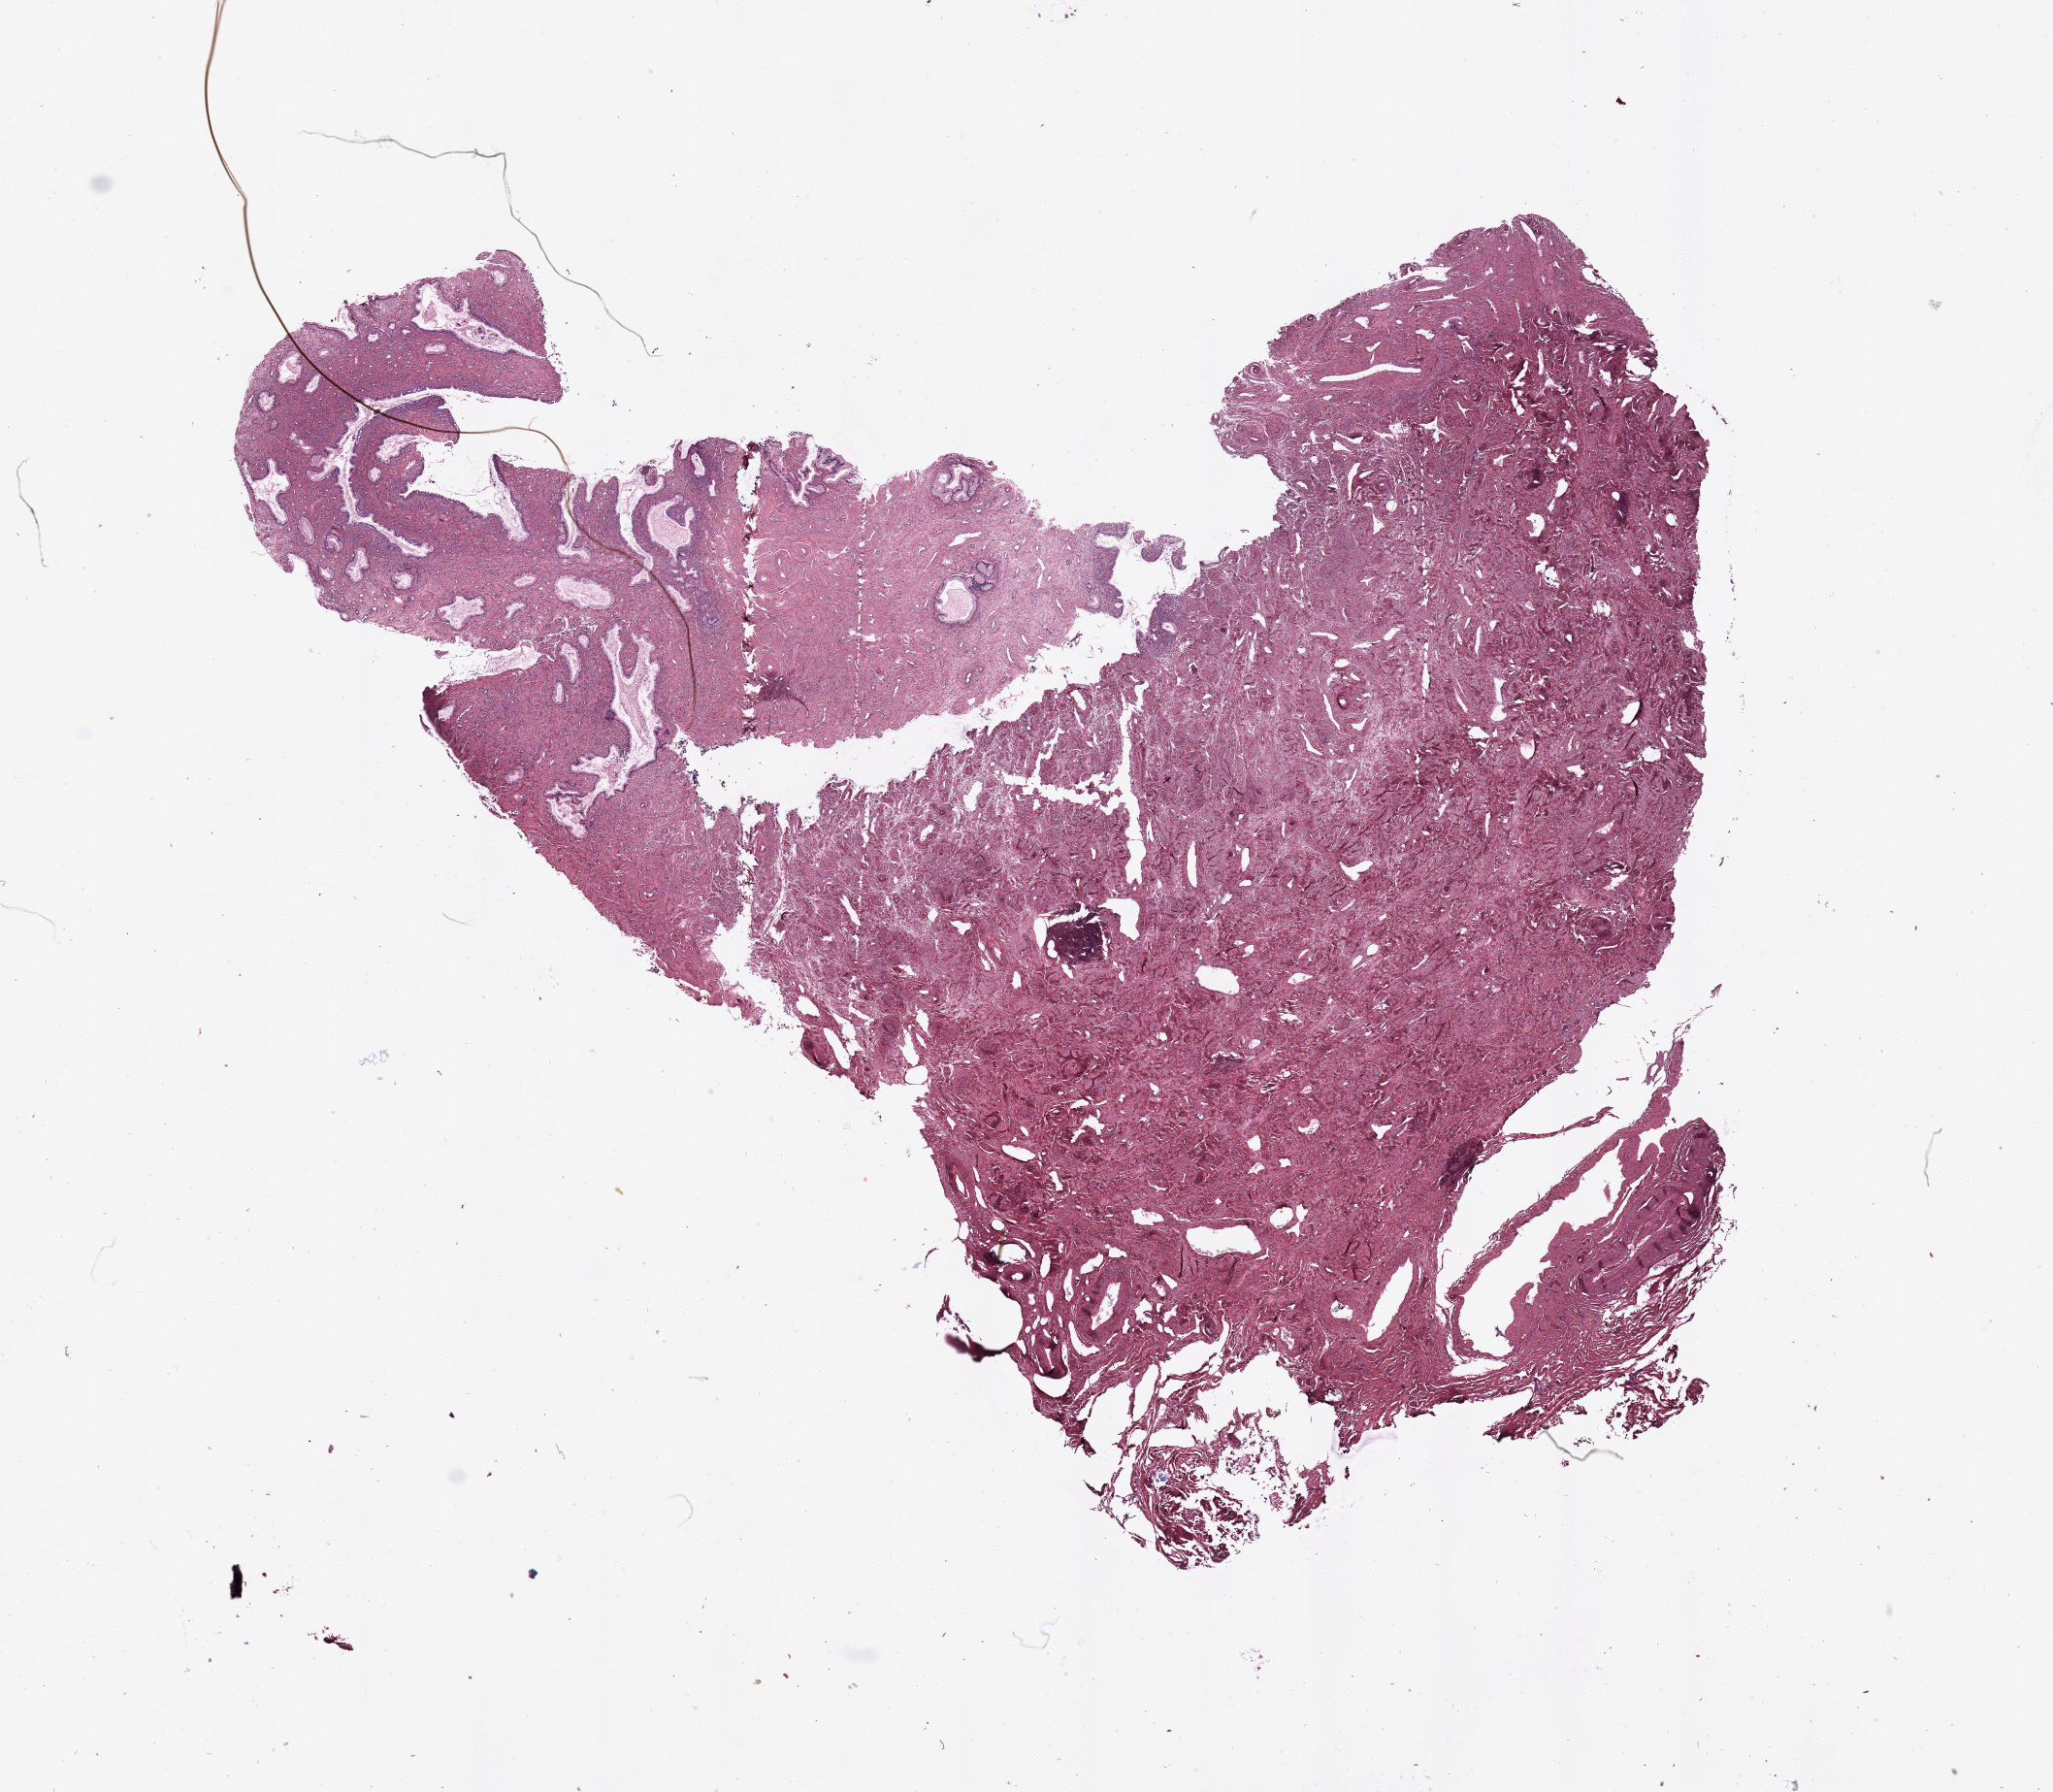
H&E whole-slide image, low-resolution overview of the scanned area, about 16.7 x 14.6 mm; uterus, normal (non-tumour) tissue. 57-year-old female patient.
- this section: normal (non-tumour) tissue from the same patient
- patient diagnosis: Endometrioid adenocarcinoma, NOS